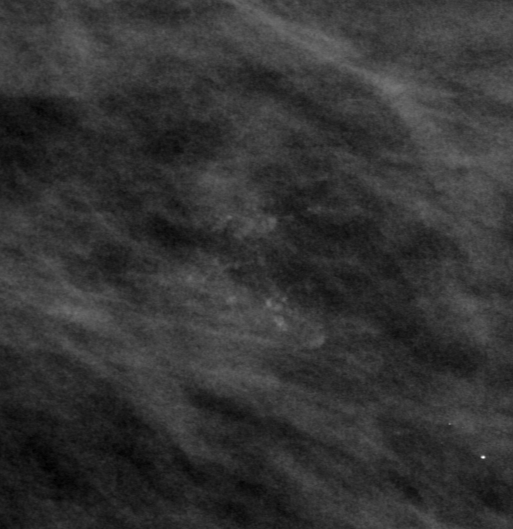
Cropped region of a digitized screen-film mammogram centred on a radiologist-marked abnormality; left breast; MLO view; BI-RADS breast density category 2 (scale 1–4).
- Finding: calcifications, morphology amorphous, distribution clustered; BI-RADS assessment category 0 (incomplete: needs additional imaging); subtlety rating 3 on a 1 (subtle) to 5 (obvious) scale; pathology (as recorded): benign.